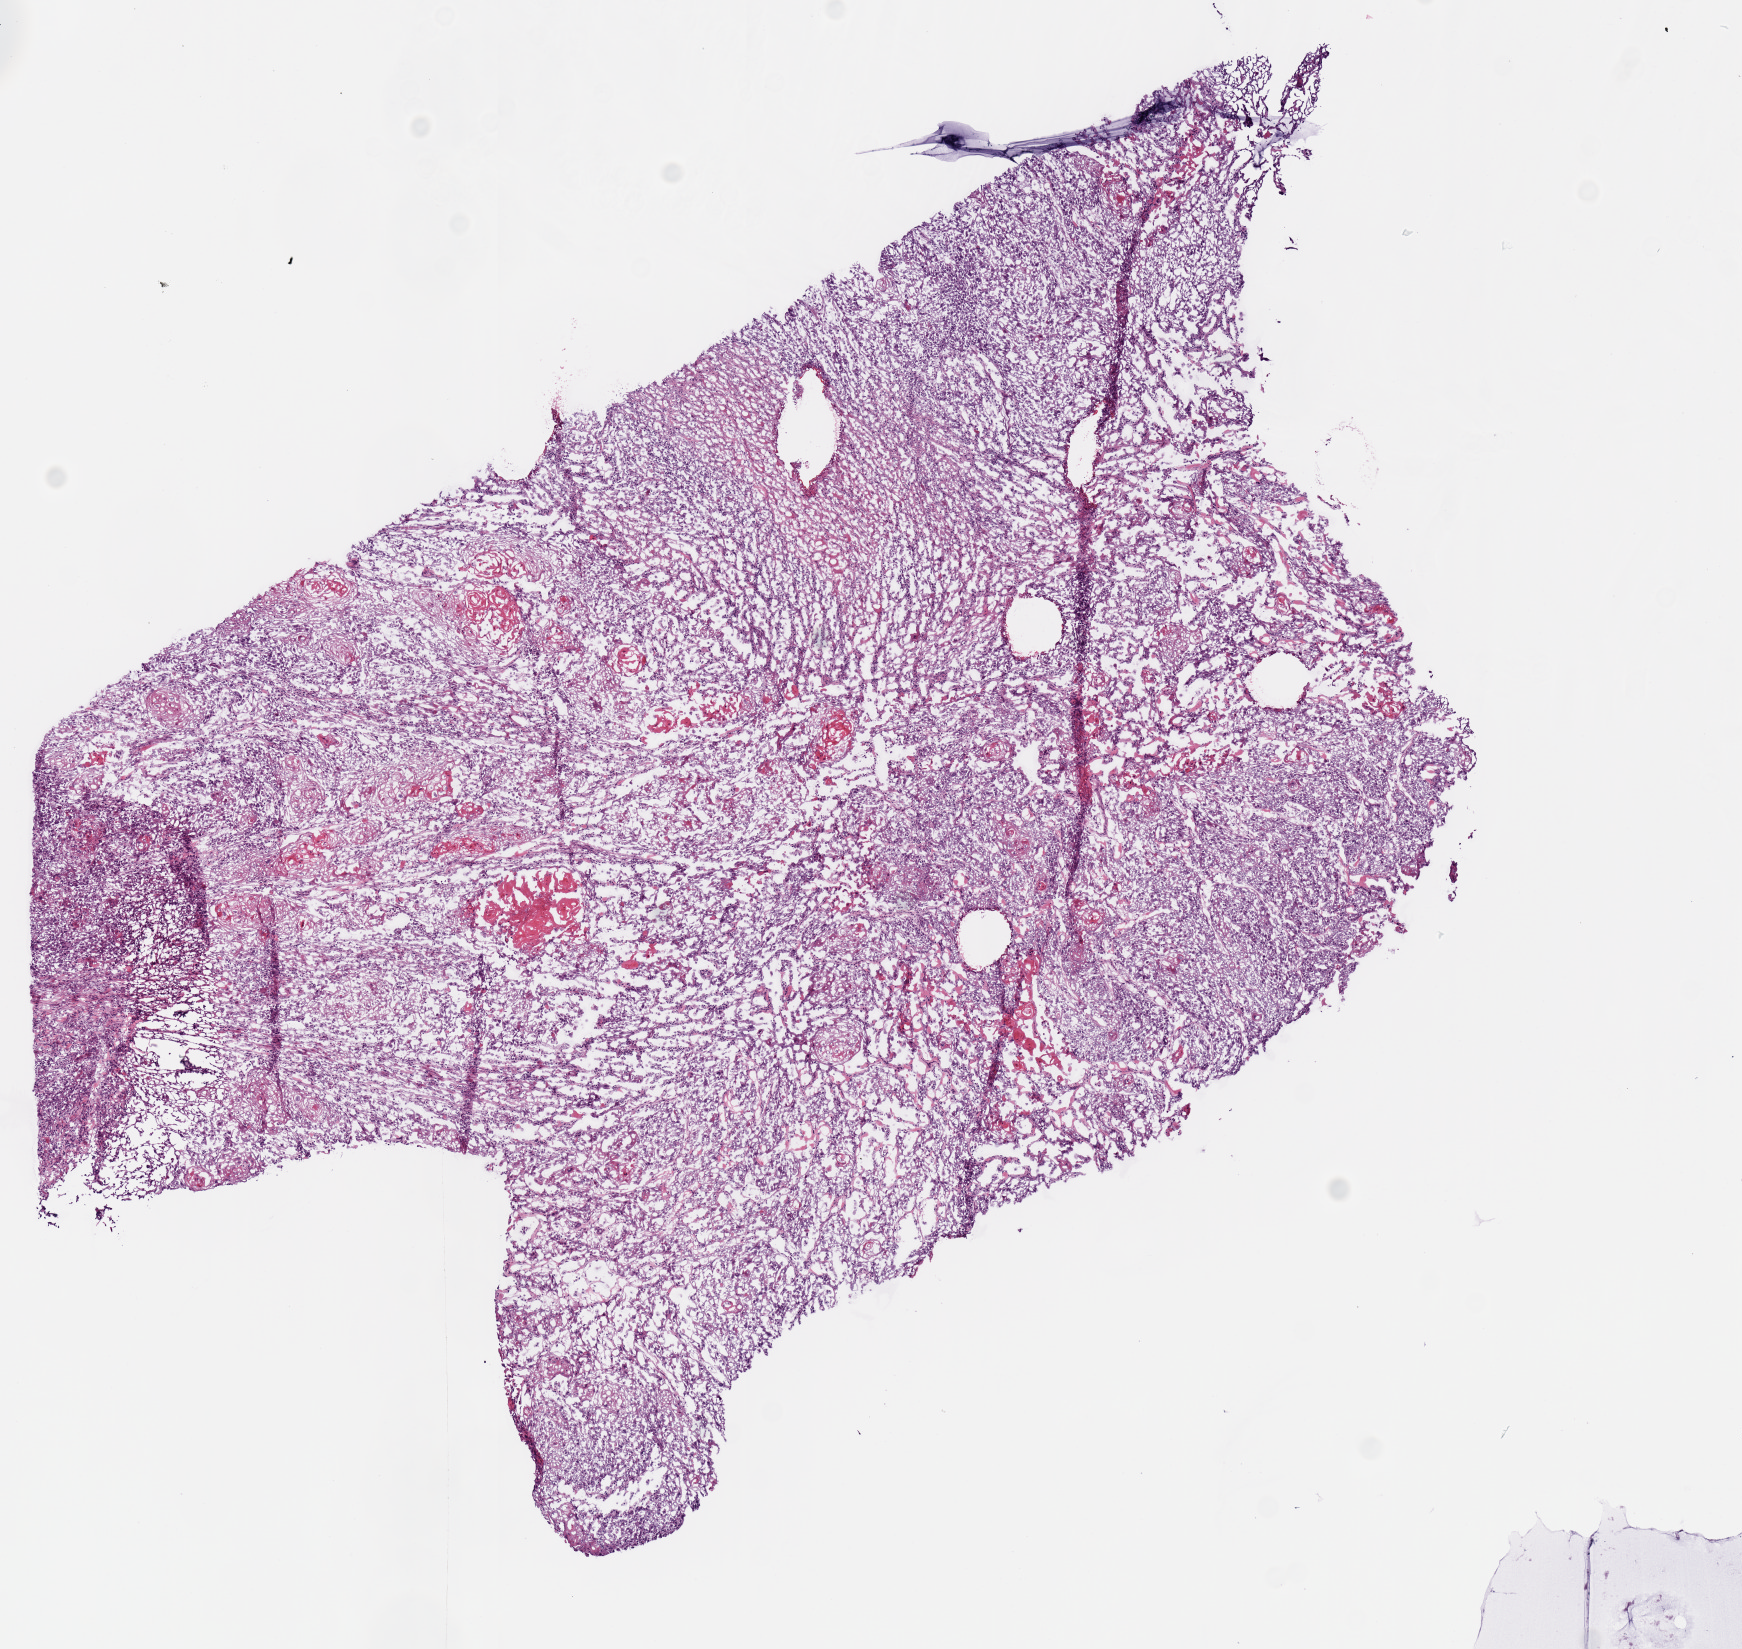
Whole-slide histology image, H&E-stained, whole scanned area (about 6.9 x 6.5 mm) shown as a low-resolution overview. Frozen section from the bottom of the tissue portion. Head and neck, primary tumour sample. Male patient; age at initial diagnosis 78 years. Histologic grade: G2 (moderately differentiated). Pathologist review of this section (percent, as recorded): tumour cells 82%, tumour nuclei 70%, normal cells 0%, stromal cells 10%, necrosis 8%.
- AJCC pathologic stage: IVA (7th edition)
- diagnosis: Squamous cell carcinoma, NOS (floor of mouth, NOS)